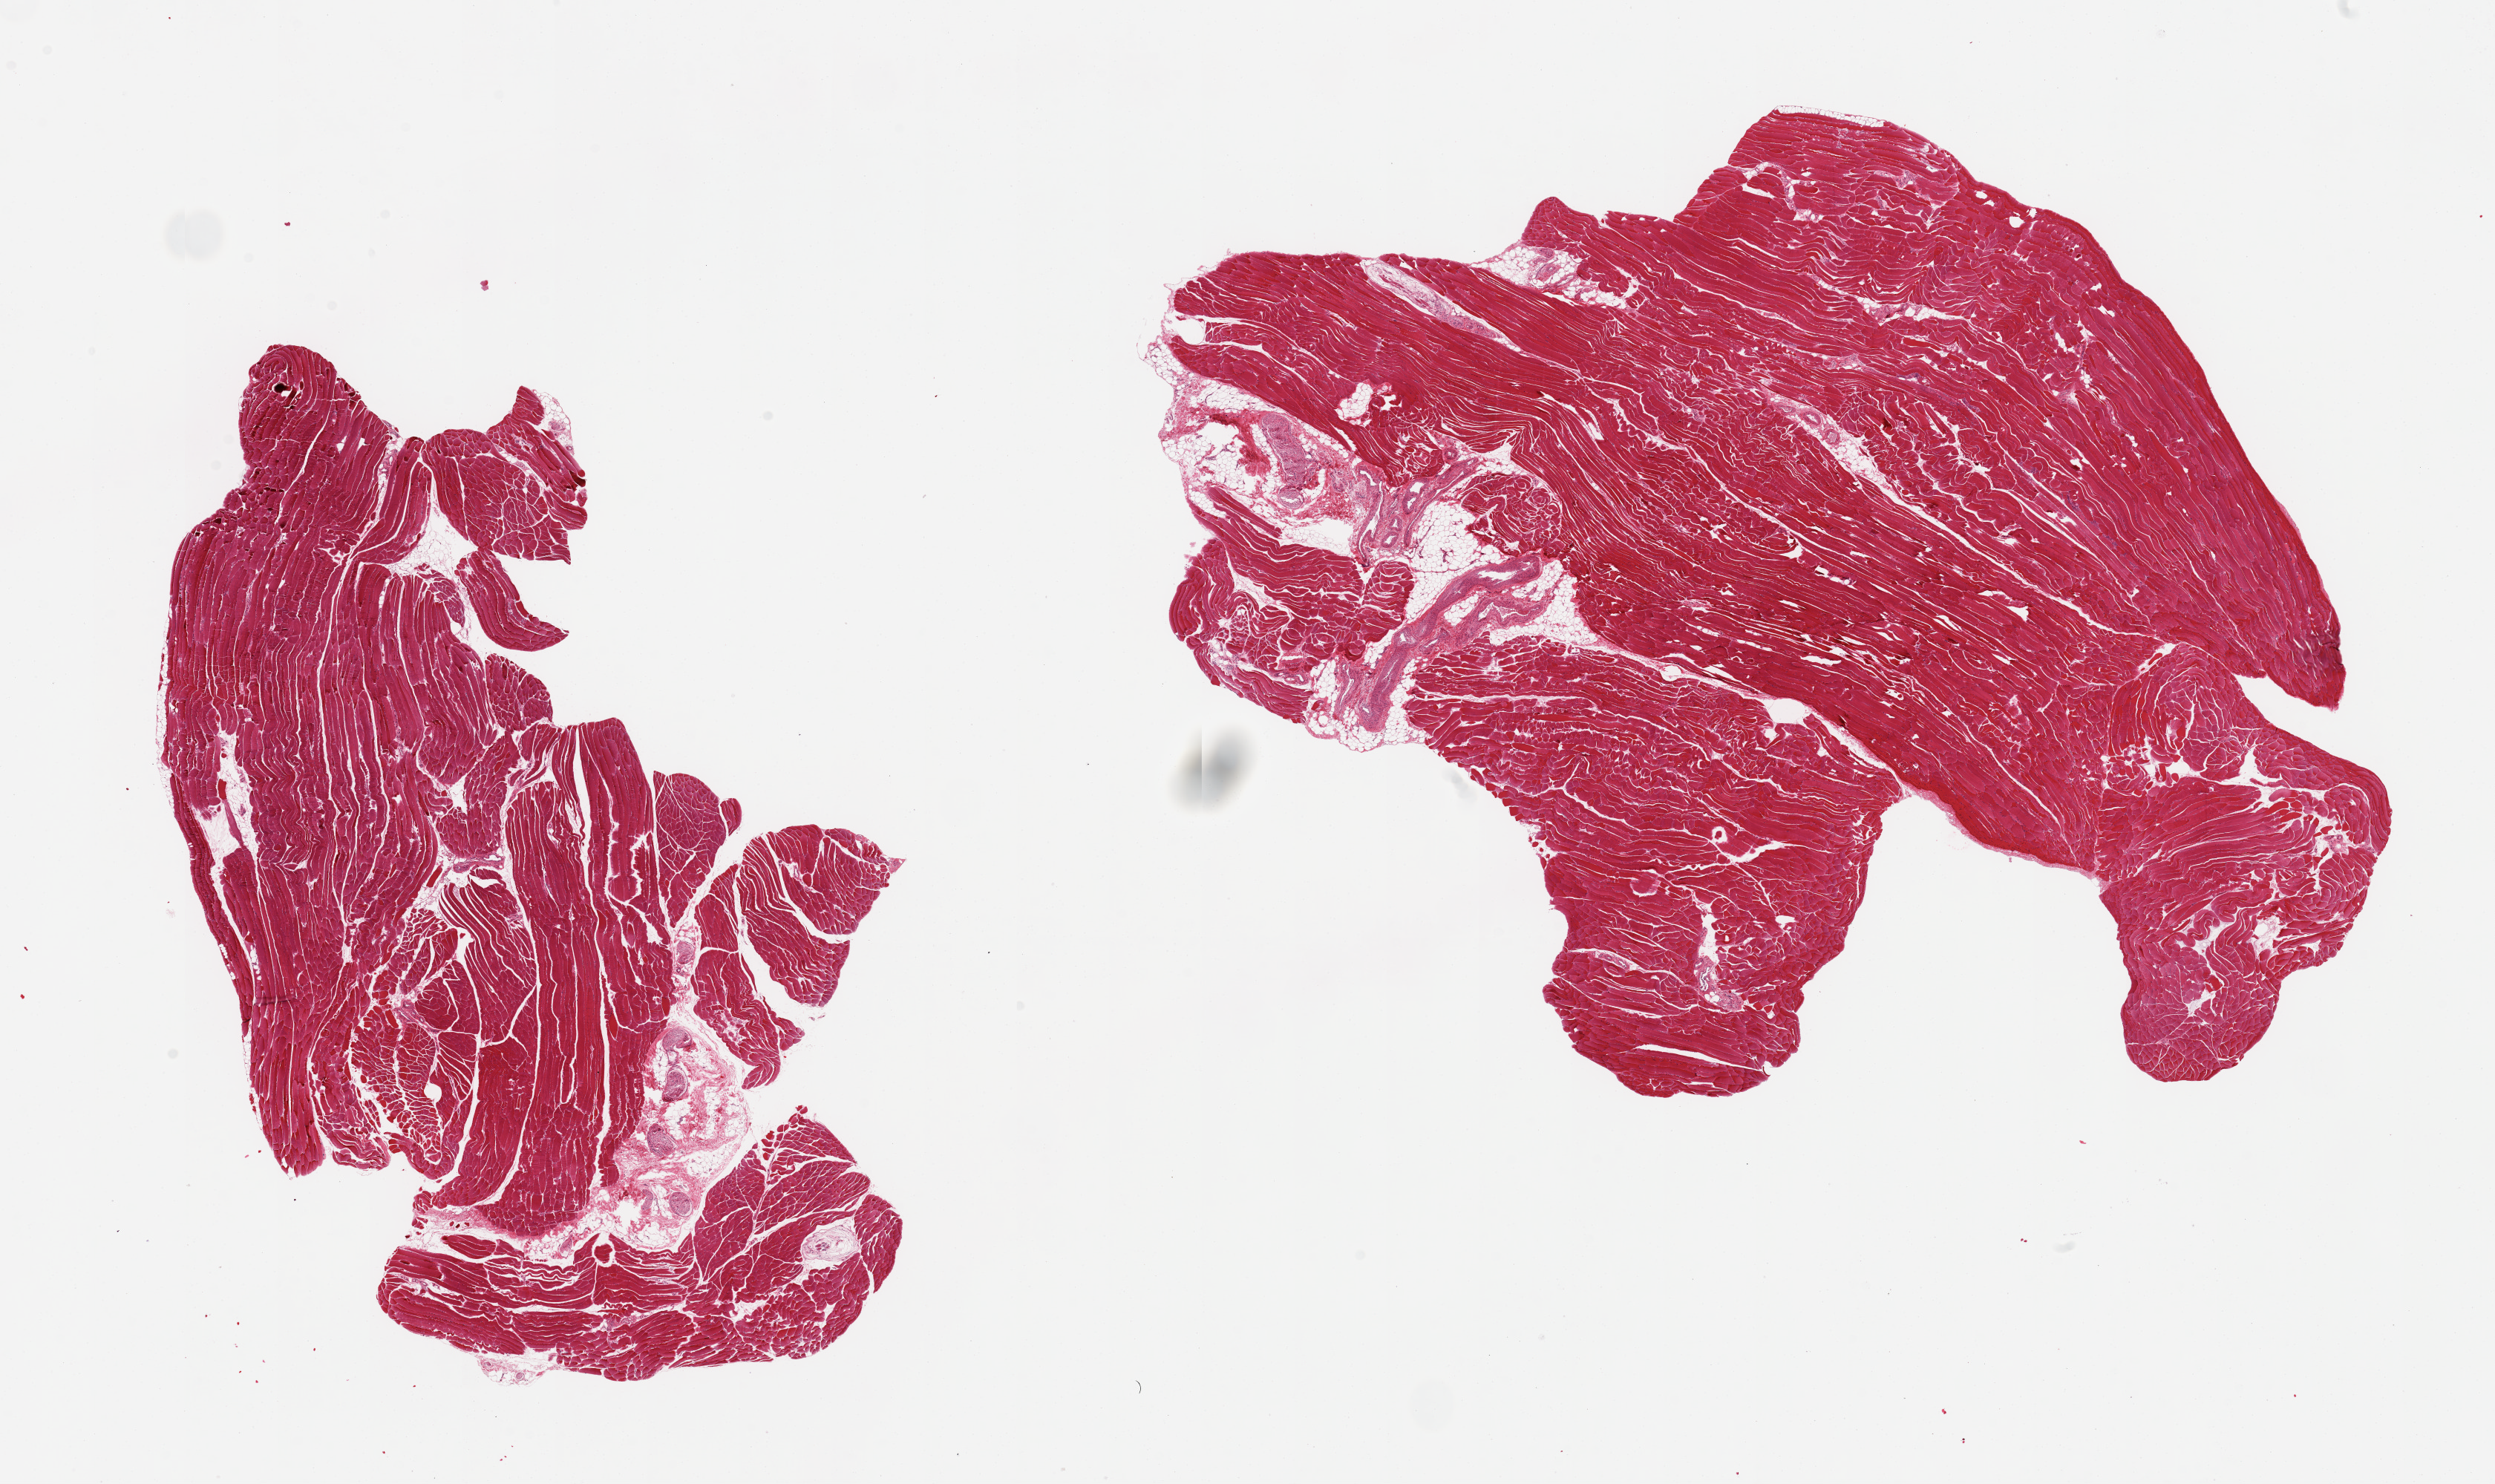
Digitized haematoxylin and eosin-stained section, low-resolution overview of the scanned area, about 26.6 x 15.8 mm. PAXgene-fixed paraffin-embedded (PFPE) section. Sampled site (target tissue): skeletal muscle. Tissue donor sample.
Pathologist's review note for this sample: 2 pieces; 5-10% is internal fat/vessels/nerve.